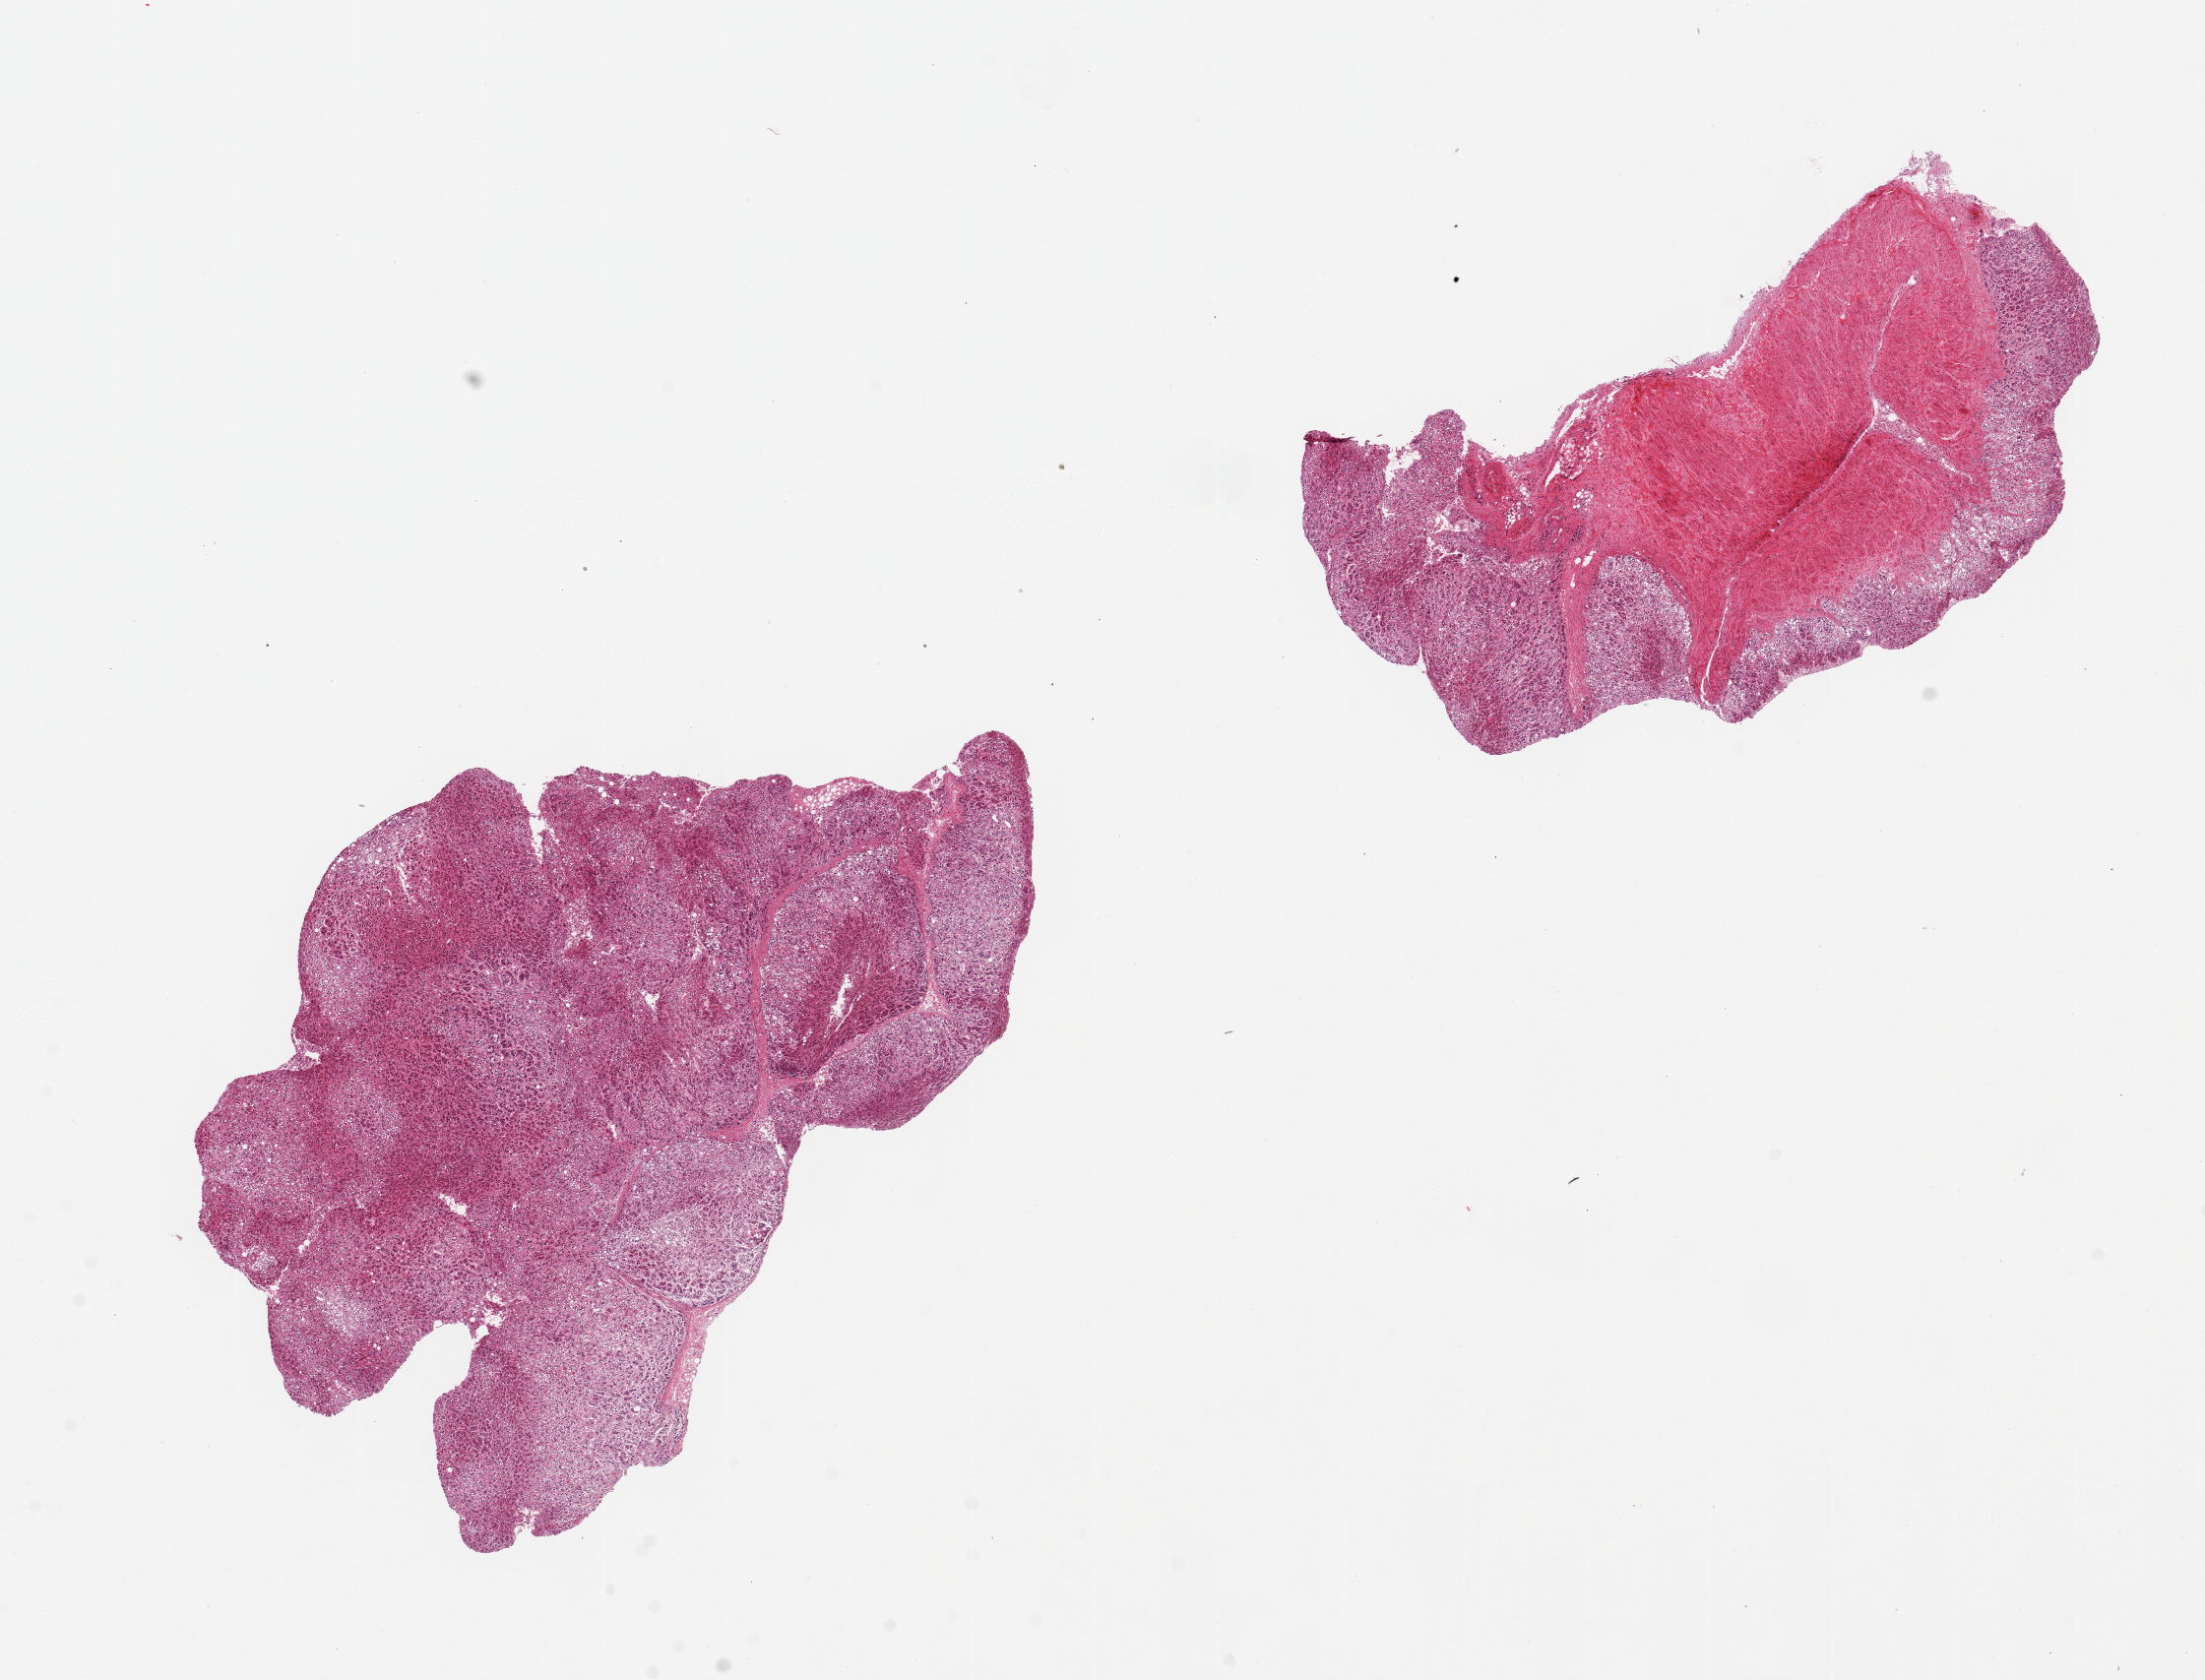
Whole-slide image, H&E stain, brightfield — shown as a low-resolution overview of the whole scanned area (about 17.7 x 13.5 mm, slide scanned at 20x); PAXgene-fixed paraffin-embedded (PFPE) section; section of adrenal gland (target tissue); tissue donor sample. Male donor.
Review note (as recorded): 2 pieces, 8x6 & 6x4mm; smaller has ~70% muscular core.